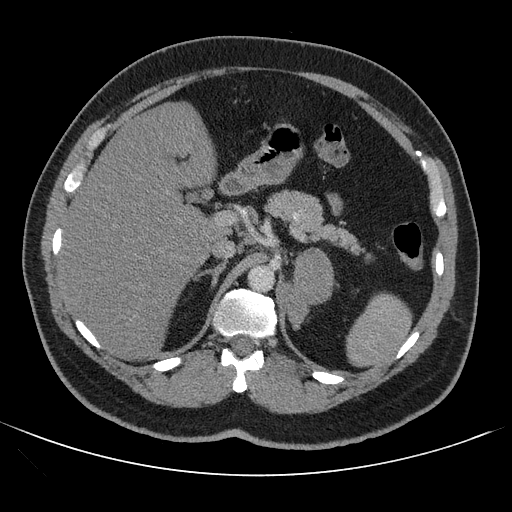
Contrast-enhanced abdominal CT, one axial slice. Position 70 of 121 along the scan axis. 120 kVp. Soft-tissue window (W 400 / L 40 HU). 512 × 512 image matrix. Male patient, age 53 years. From the clinical record (not read from this slice): diagnosis: adrenocortical carcinoma; tumour side: left adrenal; tumour size at pathology: 7.9 cm; Ki-67 index: 20 %; stage (as recorded): 2.
Annotated regions visible in this slice (semi-automatically segmented with operator editing):
- mass: box from (x=285, y=249) to (x=332, y=327) px